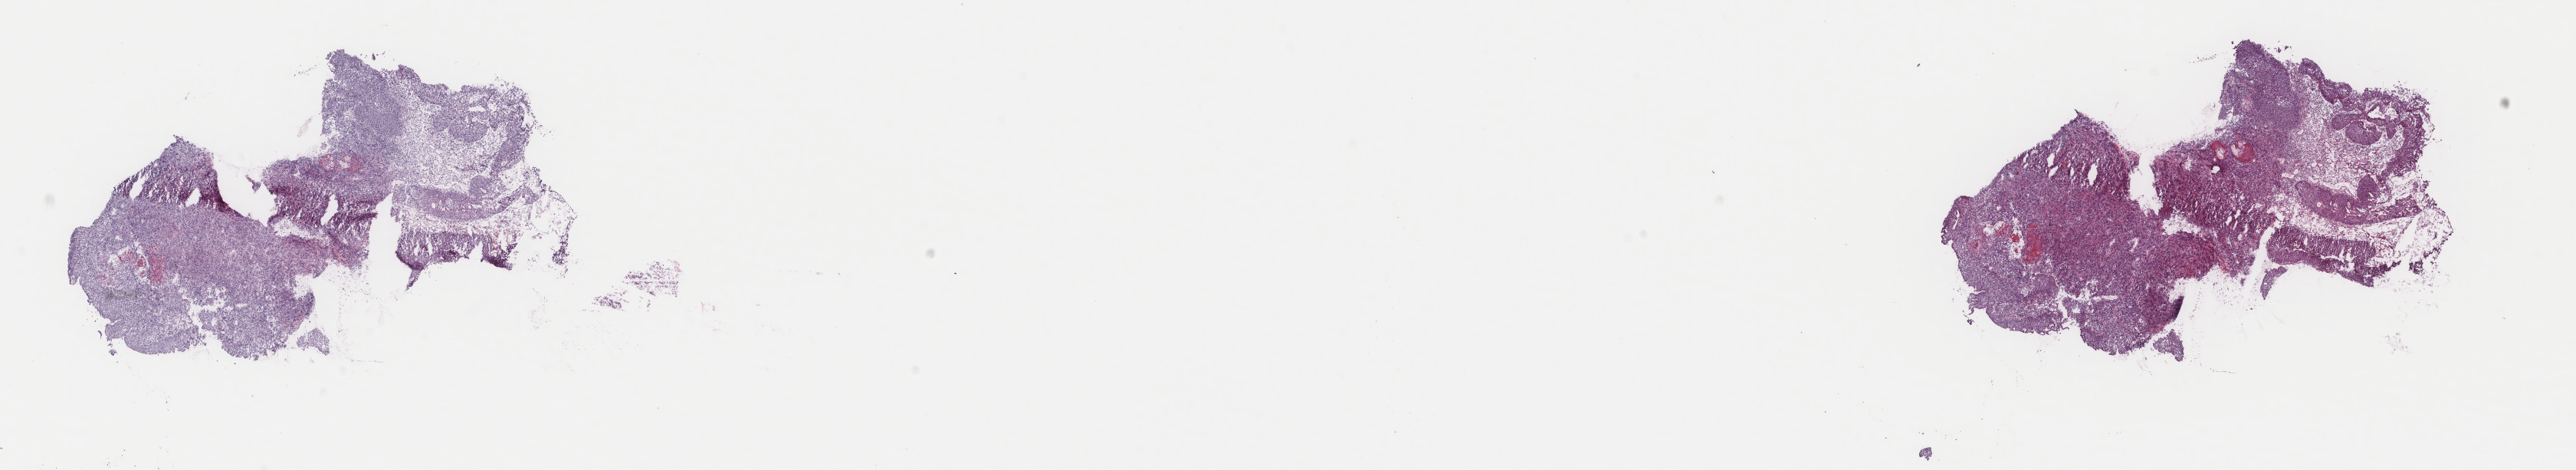
Digitized H&E tissue section (whole slide), shown as a low-resolution overview of the whole scanned area (about 26.7 x 4.9 mm, slide scanned at 40x). Frozen section. Bladder, primary tumour sample. Patient: female, age at initial diagnosis 75 years. Histologic grade: high grade. Composition of this section per pathologist review: tumour cells 80%, tumour nuclei 70%, normal cells 15%, stromal cells 5%, necrosis 0%. Inflammatory infiltration, as recorded: lymphocyte infiltration 0%, monocyte infiltration 0%, neutrophil infiltration 0%.
- AJCC pathologic stage: III (7th edition)
- pathologic diagnosis: Transitional cell carcinoma (posterior wall of bladder)
- lymph nodes positive (case pathology): 0 of 12 examined